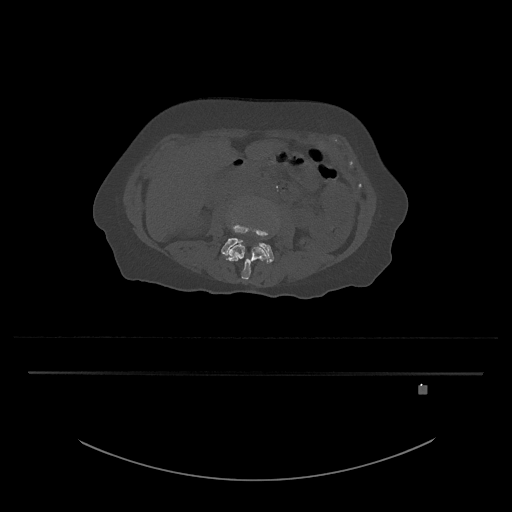
CT including the spine, one axial slice; slice 396 of 797 in the series (ordered by position); bone window (W 1800 / L 400 HU); 0.5 mm slice thickness; 512 × 512 image matrix, field of view 500 × 500 mm. Patient: female, 57 years. Case-level facts recorded for this patient, not image findings: primary cancer: cervical.
Annotated regions visible in this slice (semi-automatic segmentation, software-assisted and operator-edited):
- L3 vertebra: bounding box <225,243,267,280> (left, top, right, bottom; pixels)
- L4 vertebra: <221,213,274,264>